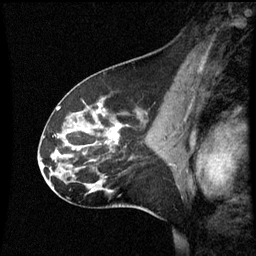
Breast MRI (dynamic contrast-enhanced), one sagittal slice; position 33 of 60 along the scan axis; dynamic contrast-enhanced series, image 2 of 3 at this slice position (ordered by acquisition); 1.5 T; TE 4.2 ms, TR 8.9 ms; 2 mm slice thickness; 256 × 256 image matrix, field of view 200 × 200 mm. Patient: female, 45 years. Case-level facts recorded for this patient, not image findings: setting: breast cancer imaged before/during neoadjuvant chemotherapy; receptor status: HR-positive, HER2-negative.
Outlined on this slice (semi-automatic segmentation, software-assisted and operator-edited):
- analysis volume of interest (the breast-tissue region the enhancement analysis was run in; not a lesion): box from (x=46, y=94) to (x=171, y=205) px
- tumour enhancement mask (voxels above the 70 % enhancement threshold inside the analysis volume of interest): (x=58, y=104)–(x=121, y=145)